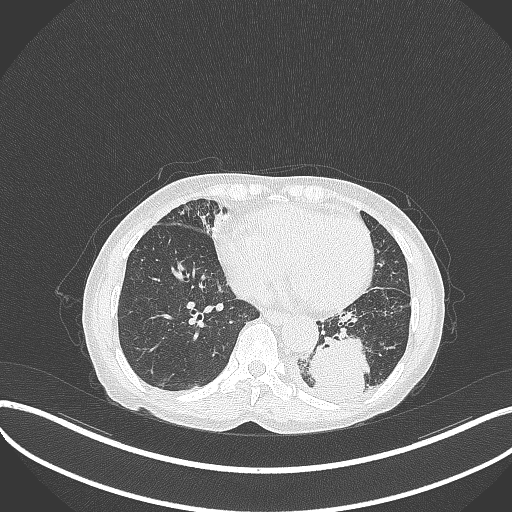
Chest CT, one axial slice; slice 99 of 370 in the series (ordered by position); 120 kVp; lung window (W 1500 / L -600 HU); 1 mm slice thickness; 512 × 512 image matrix, field of view 400 × 400 mm. Patient: female, 78 years. Case-level facts recorded for this patient, not image findings: clinical TNM (as recorded): T3 N0 M1.
Annotated regions visible in this slice (bounding box drawn by a radiologist):
- lung tumour (recorded histology: squamous cell carcinoma): box from (x=306, y=328) to (x=373, y=397) px